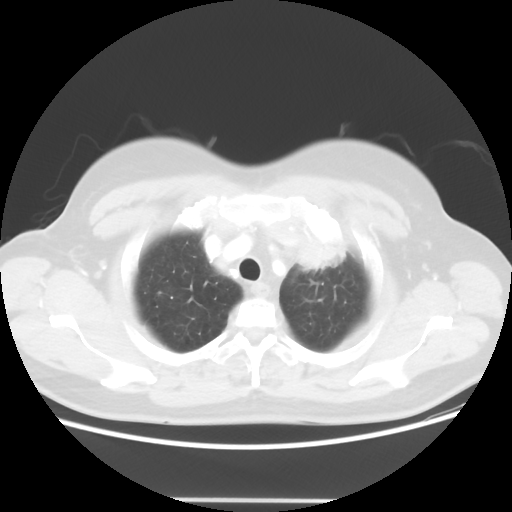
Chest CT, one axial slice. Slice 46 of 52 in the series (ordered by position). 120 kVp. Lung window (W 1500 / L -600 HU). 5 mm slice thickness. 512 × 512 image matrix, field of view 382 × 382 mm. Female patient, age 52 years. From the clinical record (not read from this slice): clinical TNM (as recorded): T2 N3 M0.
Outlined on this slice (bounding box drawn by a radiologist):
- lung tumour (recorded histology: adenocarcinoma): bounding box (x1, y1, x2, y2) in pixels: (290, 226, 348, 277)